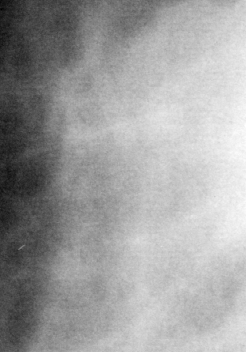
Region of interest cut from a scanned film mammogram (one marked finding), right breast, MLO view.
Marked abnormality: mass, shape oval, margins obscured; BI-RADS assessment category 4; subtlety rating 4 on a 1 (subtle) to 5 (obvious) scale; pathology (as recorded): benign.